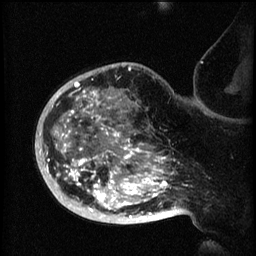
Breast MRI (dynamic contrast-enhanced), one sagittal slice; position 47 of 60 along the scan axis; 3 images stored at this slice position (order not interpretable as contrast timing); 1.5 T; TE 4.2 ms, TR 8.2 ms; 2 mm slice thickness; 256 × 256 image matrix, field of view 200 × 200 mm. Patient: female, 50 years.
Outlined on this slice (semi-automatically segmented with operator editing):
- analysis volume of interest (the breast-tissue region the enhancement analysis was run in; not a lesion): bounding box [x1, y1, x2, y2] px = [44, 72, 173, 219]
- tumour enhancement mask (voxels above the 70 % enhancement threshold inside the analysis volume of interest): [47, 82, 173, 219]